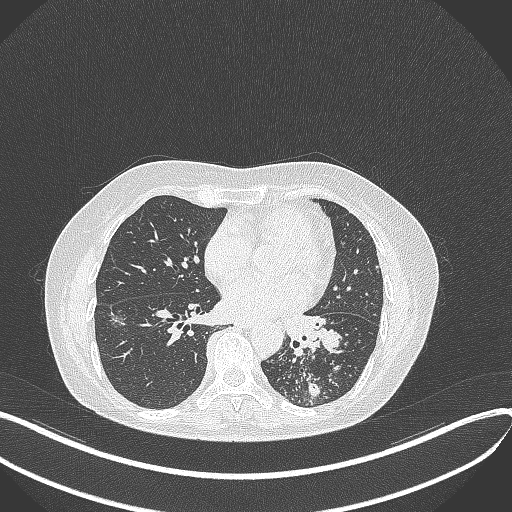
Chest CT, one axial slice; position 177 of 429 along the scan axis; reconstruction kernel B70f; lung window (W 1500 / L -600 HU); 1 mm slice thickness; 512 × 512 image matrix. Patient: female, 63 years. From the clinical record (not read from this slice): clinical TNM (as recorded): T1b N0 M0; histopathological grade: G2-3.
Outlined on this slice (bounding box drawn by a radiologist):
- lung tumour (recorded histology: adenocarcinoma): bounding box <283,308,348,364> (left, top, right, bottom; pixels)